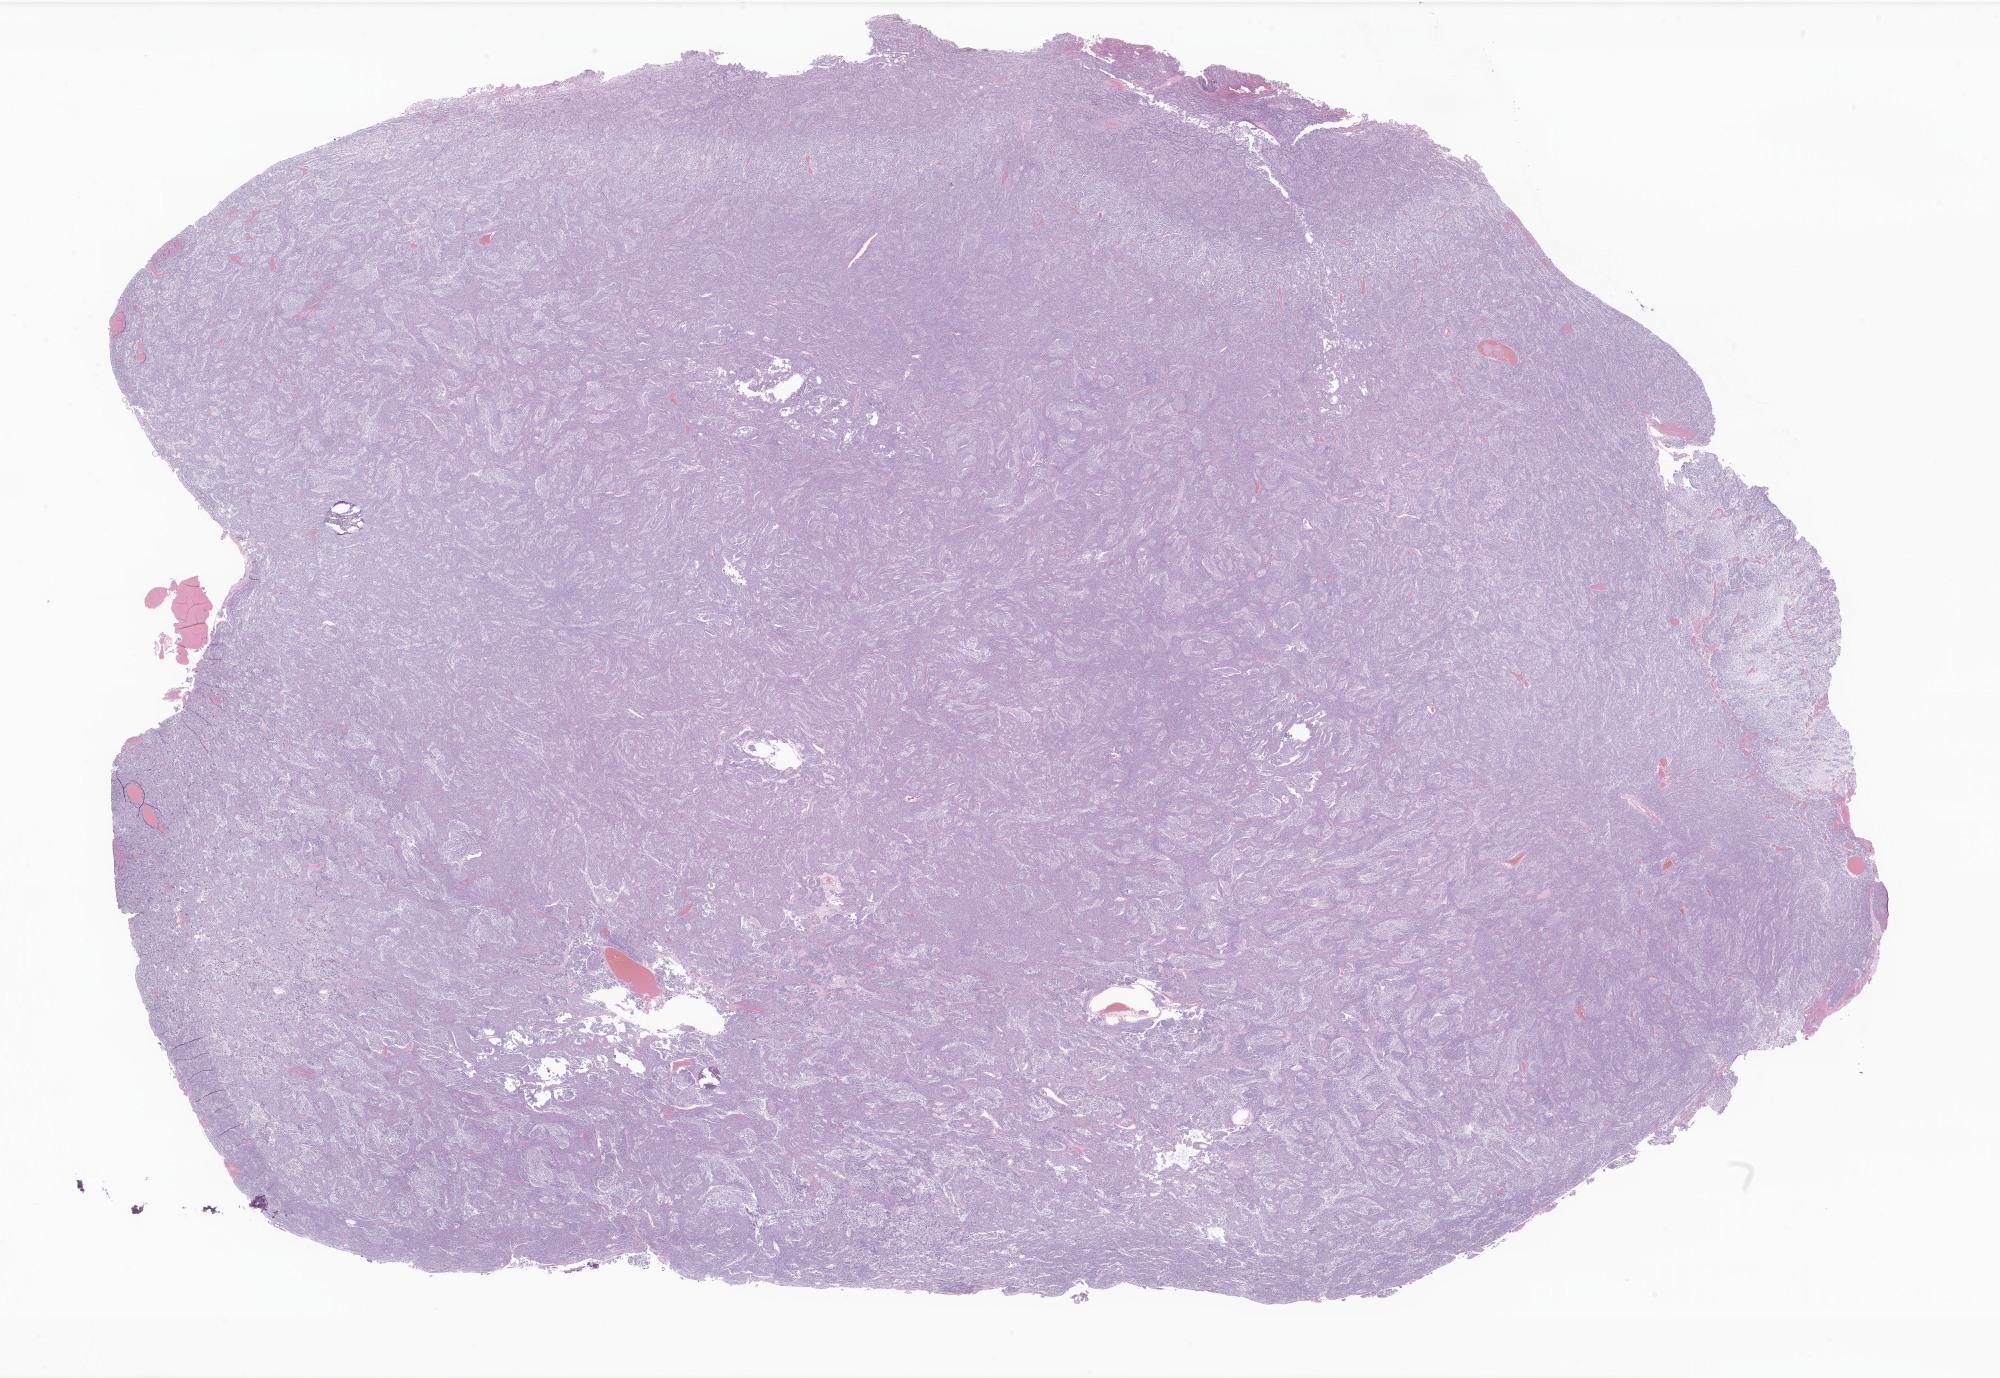
Whole-slide image, haematoxylin and eosin stain of tumor tissue from the brain — shown as a low-resolution overview of the whole scanned area (about 33.7 x 23.2 mm), formalin-fixed, paraffin-embedded (FFPE) tissue. Patient female; age 550 days (about 1.5 years).
Diagnosis: Medulloblastoma, NOS.